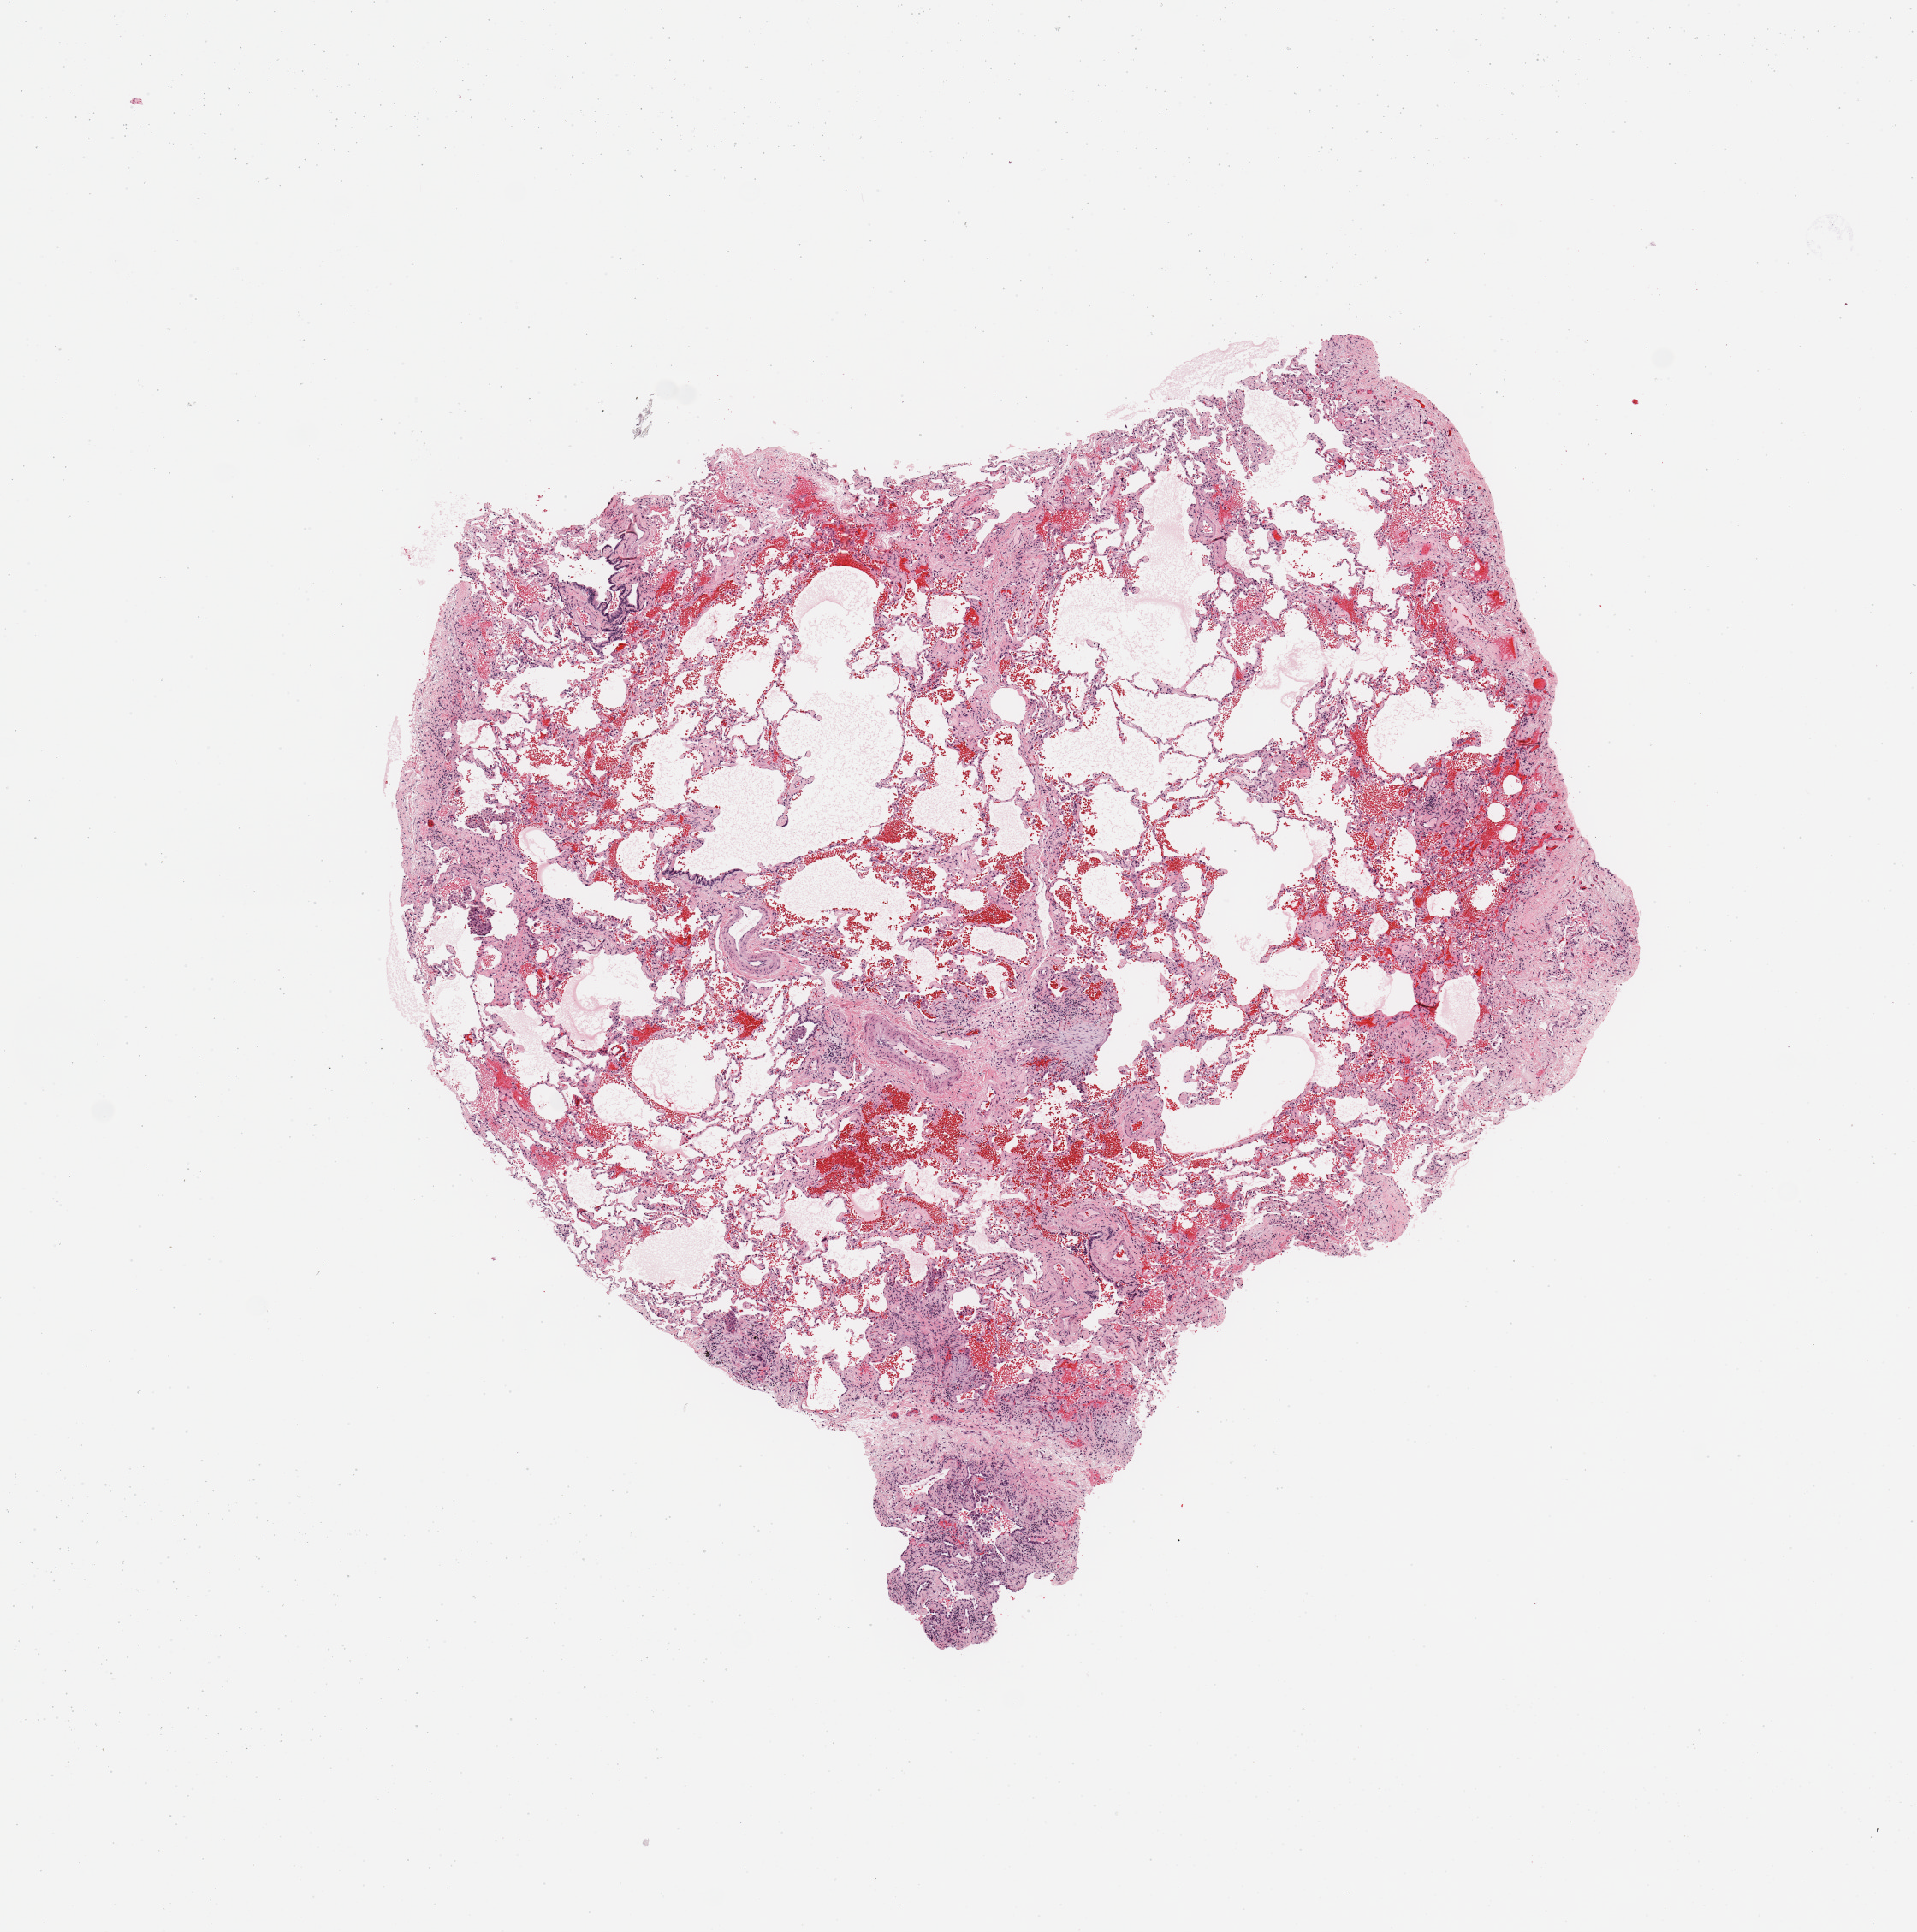
H&E-stained whole-slide image, shown as a low-resolution overview of the whole scanned area (about 8.9 x 8.9 mm, acquisition: 20x scan); normal (non-tumour) tissue sample, sampled site: lung. Male, 68 y/o.
This section: normal (non-tumour) tissue from the same patient. Patient diagnosis: Squamous cell carcinoma, NOS.